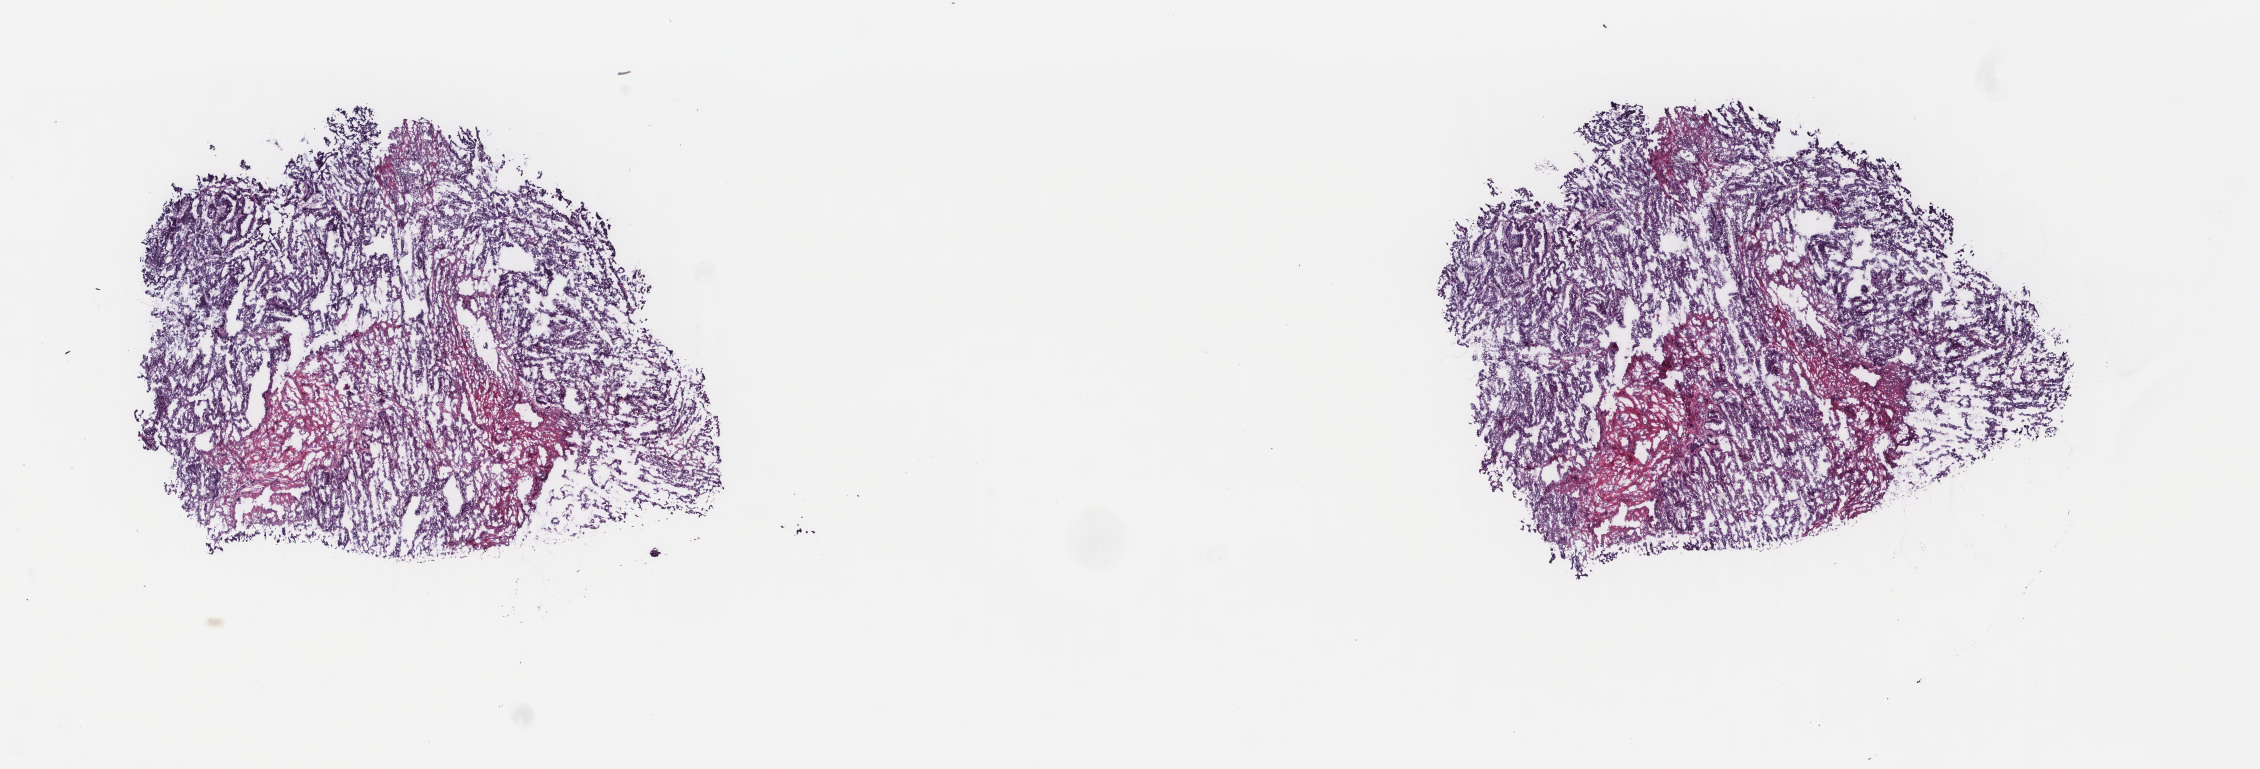
Hematoxylin and eosin (H&E) stained whole-slide image — low-resolution overview of the scanned area, about 17.9 x 6.1 mm, frozen section from the top of the tissue portion, uterus, primary tumour sample. Female, age 63 years at initial diagnosis. Histologic grade: G2 (moderately differentiated). Pathologist review of this section (percent, as recorded): tumour cells 60%, tumour nuclei 60%, normal cells 0%, stromal cells 30%, necrosis 10%. Inflammatory infiltration, as recorded: lymphocyte infiltration 40%, monocyte infiltration 20%, neutrophil infiltration 20%.
- FIGO stage: IIB
- histologic diagnosis: Endometrioid adenocarcinoma, NOS (endometrium)